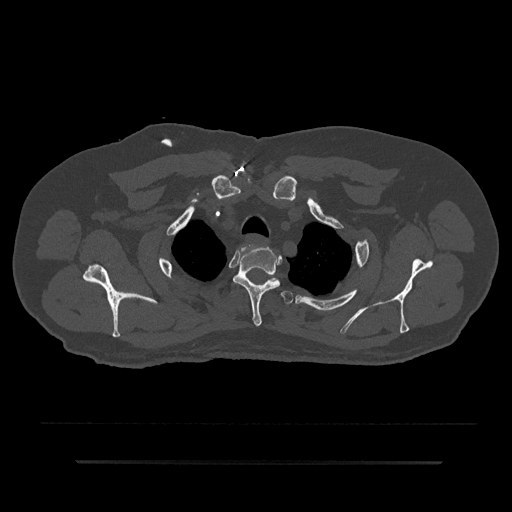
CT including the spine, one axial slice; position 693 of 797 along the scan axis; reconstruction kernel Br40s/3; 120 kVp; bone window (W 1800 / L 400 HU); 512 × 512 image matrix, field of view 464 × 464 mm. Male patient, age 59 years. From the clinical record (not read from this slice): primary cancer: bile ducts.
Annotated regions visible in this slice (semi-automatic segmentation, software-assisted and operator-edited):
- T1 vertebra: bounding box (x1, y1, x2, y2) in pixels: (240, 247, 245, 252)
- T2 vertebra: (233, 246, 280, 326)
- T3 vertebra: (280, 291, 293, 305)